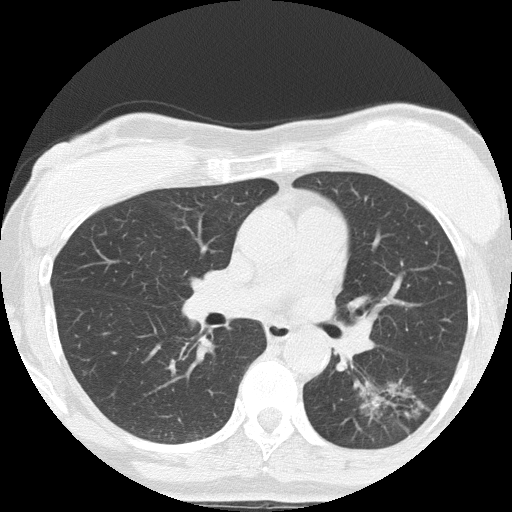
Low-dose screening chest CT, axial slice; third screening round (two years after baseline); lung window (W 1500 / L -600 HU); lung (sharp) reconstruction kernel (FC51); slice 69 of 152 in the series. Female participant, aged 64 years at enrolment. Former smoker at enrolment.
Lesion marked by an expert reader, bounding box <364,367,454,442> (left, top, right, bottom; pixels). The screening reader recorded 3 non-calcified nodules or masses ≥4 mm on this exam (right upper lobe, left lower lobe, right middle lobe); which of them this box marks is not recorded. Lung cancer was diagnosed 212 days after this screen: adenocarcinoma, NOS, left lower lobe, moderately differentiated (G2), stage IA (AJCC 6th edition), 17 mm at pathology.